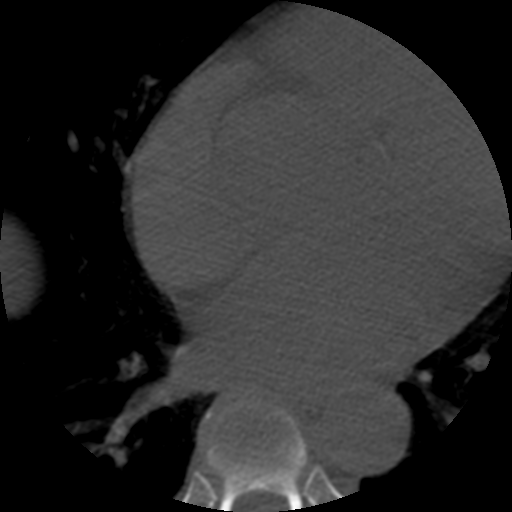
CT including the spine, one axial slice; position 341 of 508 along the scan axis; 120 kVp; bone window (W 1800 / L 400 HU); 1.25 mm slice thickness; 512 × 512 image matrix. Patient age 57 years. Case-level facts recorded for this patient, not image findings: primary cancer: prostate.
Annotated regions visible in this slice (semi-automatically segmented with operator editing):
- T6 vertebra: box from (x=211, y=401) to (x=259, y=420) px
- T7 vertebra: (x=206, y=401)–(x=308, y=512)